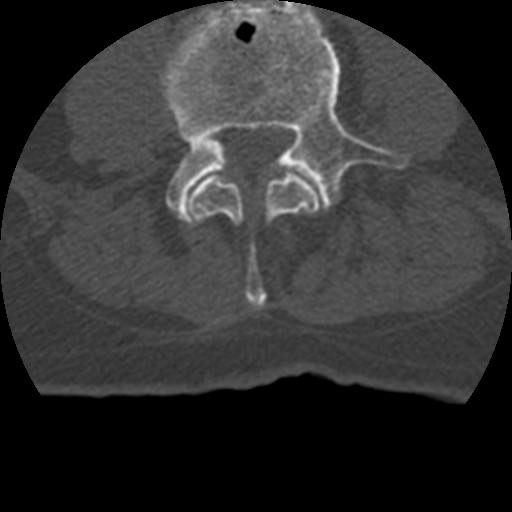
CT including the spine, one axial slice; slice 74 of 399 in the series (ordered by position); bone window (W 1800 / L 400 HU); 1.25 mm slice thickness; 512 × 512 image matrix, field of view 160 × 160 mm. Patient age 69 years. From the clinical record (not read from this slice): primary cancer: prostate.
Annotated regions visible in this slice (semi-automatically segmented with operator editing):
- L3 vertebra: bounding box (x1, y1, x2, y2) in pixels: (189, 173, 321, 309)
- L4 vertebra: (160, 0, 413, 223)